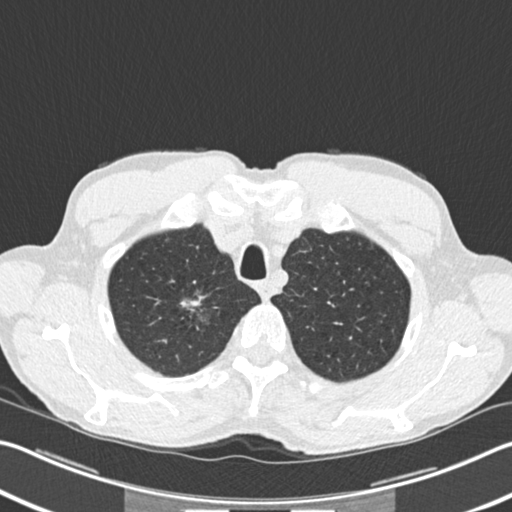
Low-dose screening chest CT, one axial slice; slice 189 of 220 in the series (ordered by position); reconstruction kernel B30f; lung window (W 1500 / L -600 HU); 2 mm slice thickness; 512 × 512 image matrix, field of view 342 × 342 mm.
Outlined on this slice (outlined manually by an expert reader):
- lesion 1 (tumor, upper lobe of right lung): bounding box [x1, y1, x2, y2] px = [181, 300, 200, 310]